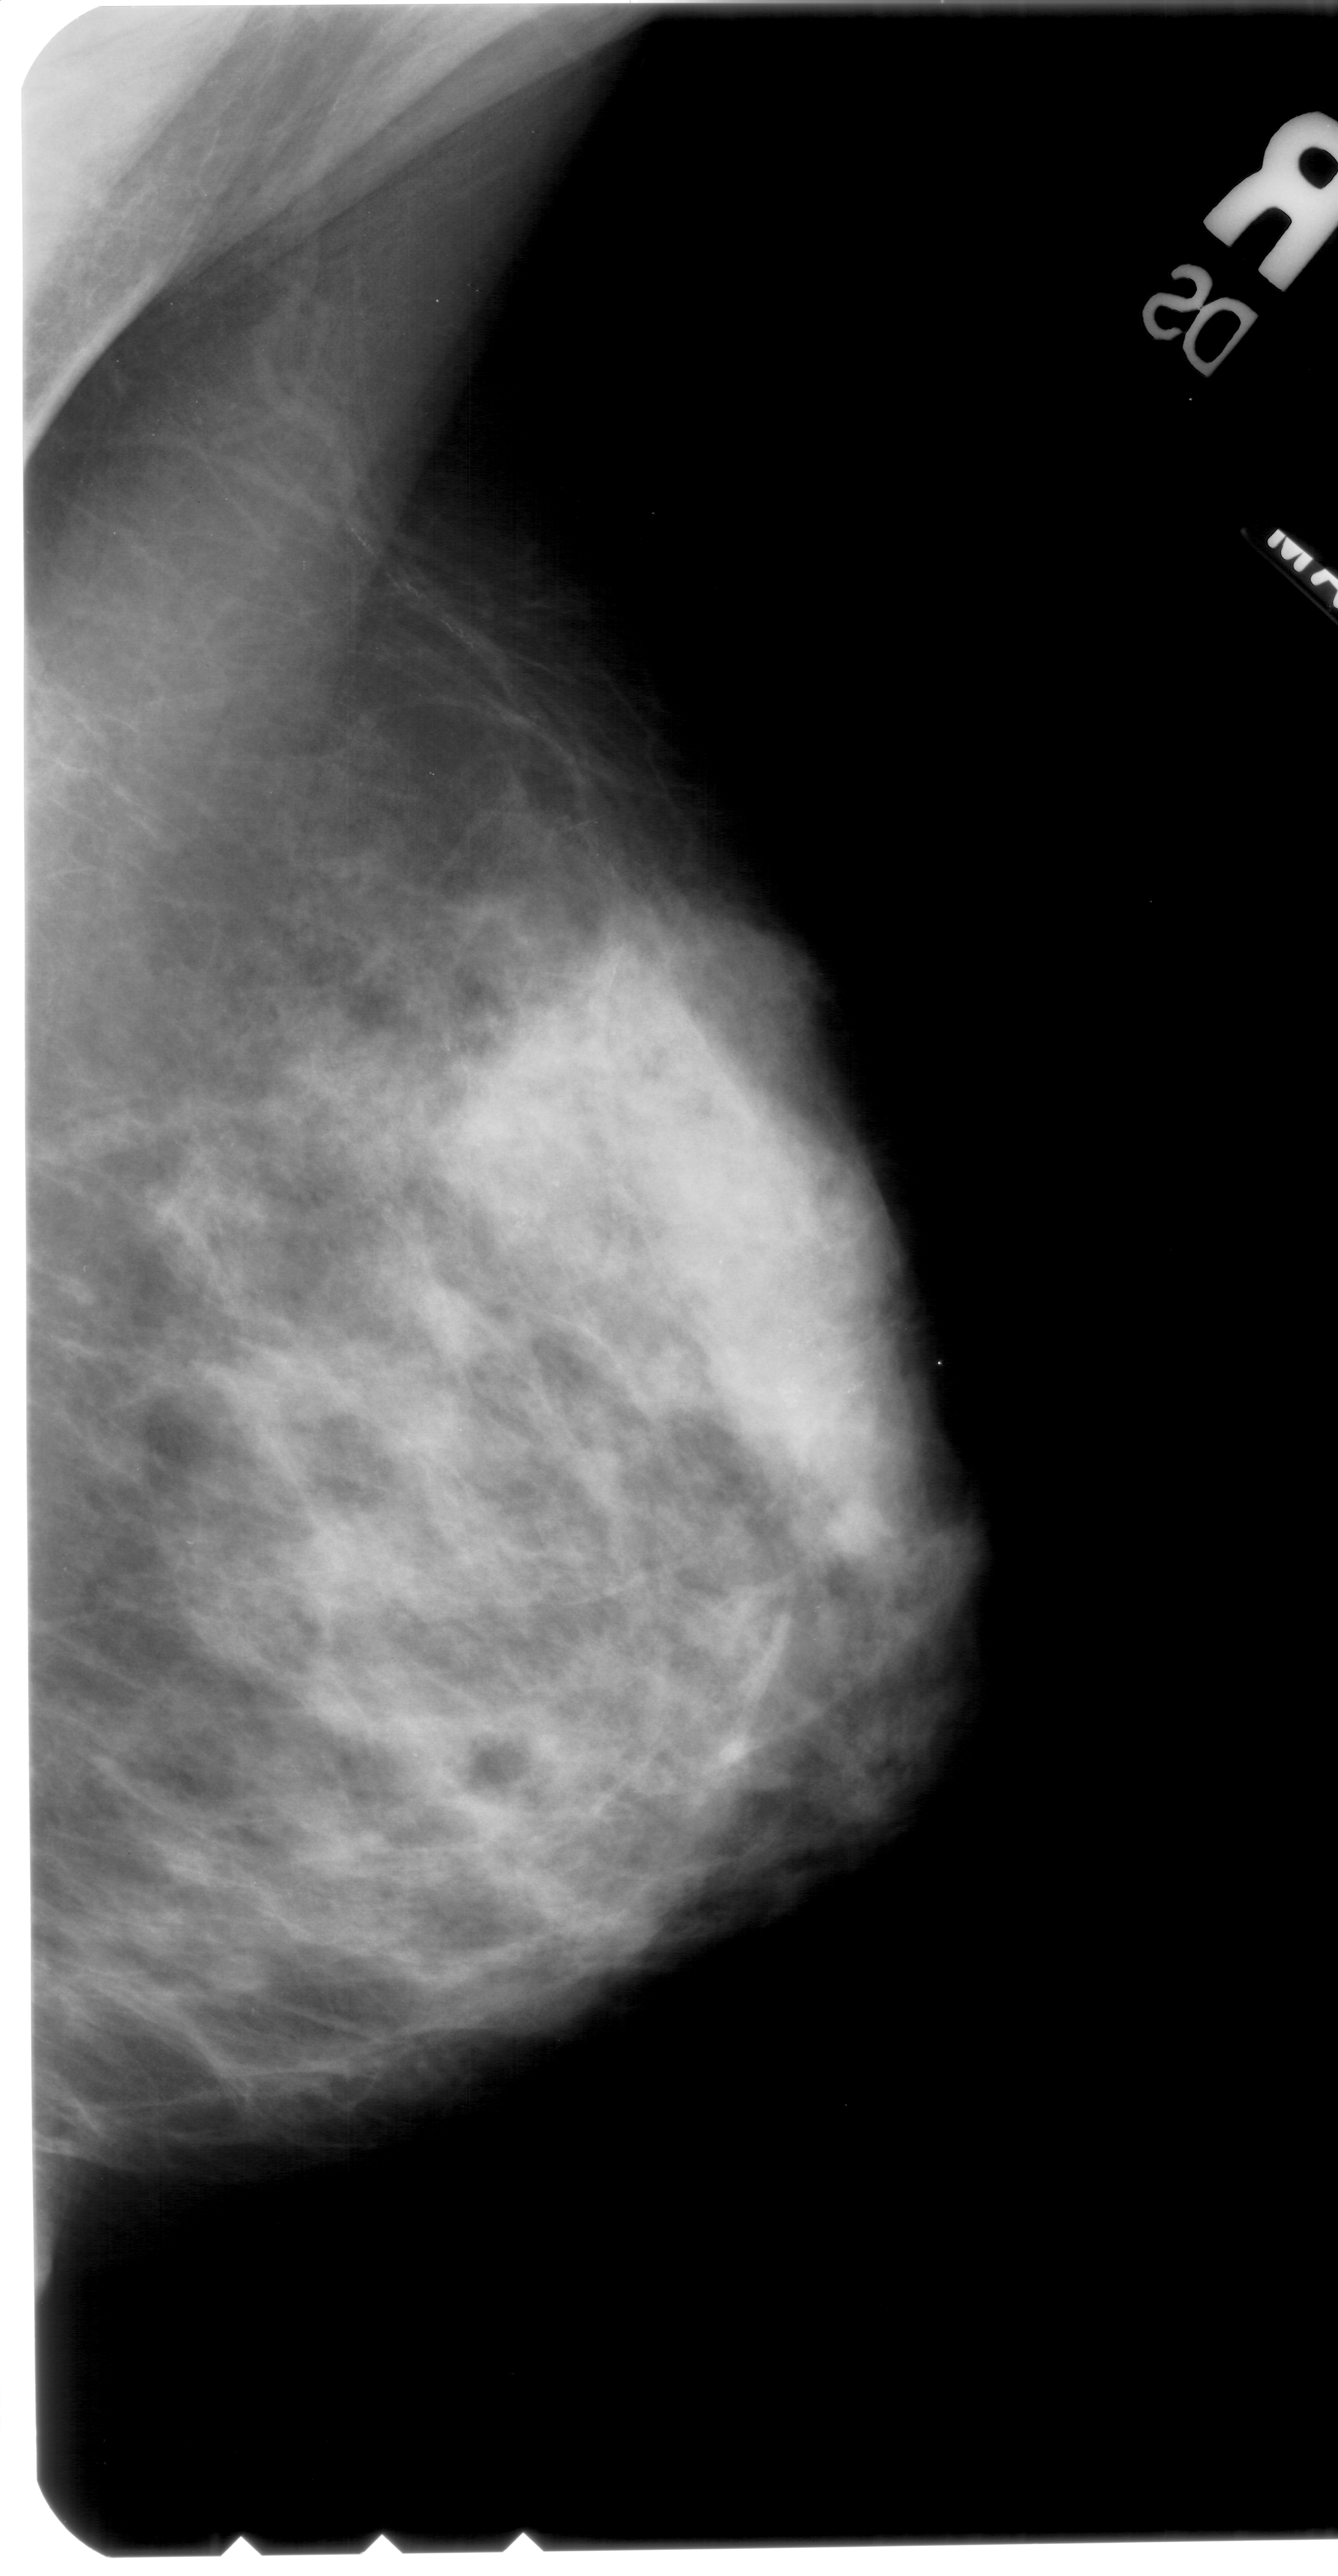
Scanned film-screen mammogram; right breast; mediolateral oblique (MLO) view.
Radiologist-marked abnormalities on this image: calcifications, morphology pleomorphic, distribution segmental; BI-RADS assessment category 4; subtlety rating 1 on a 1 (subtle) to 5 (obvious) scale; pathology (as recorded): malignant.